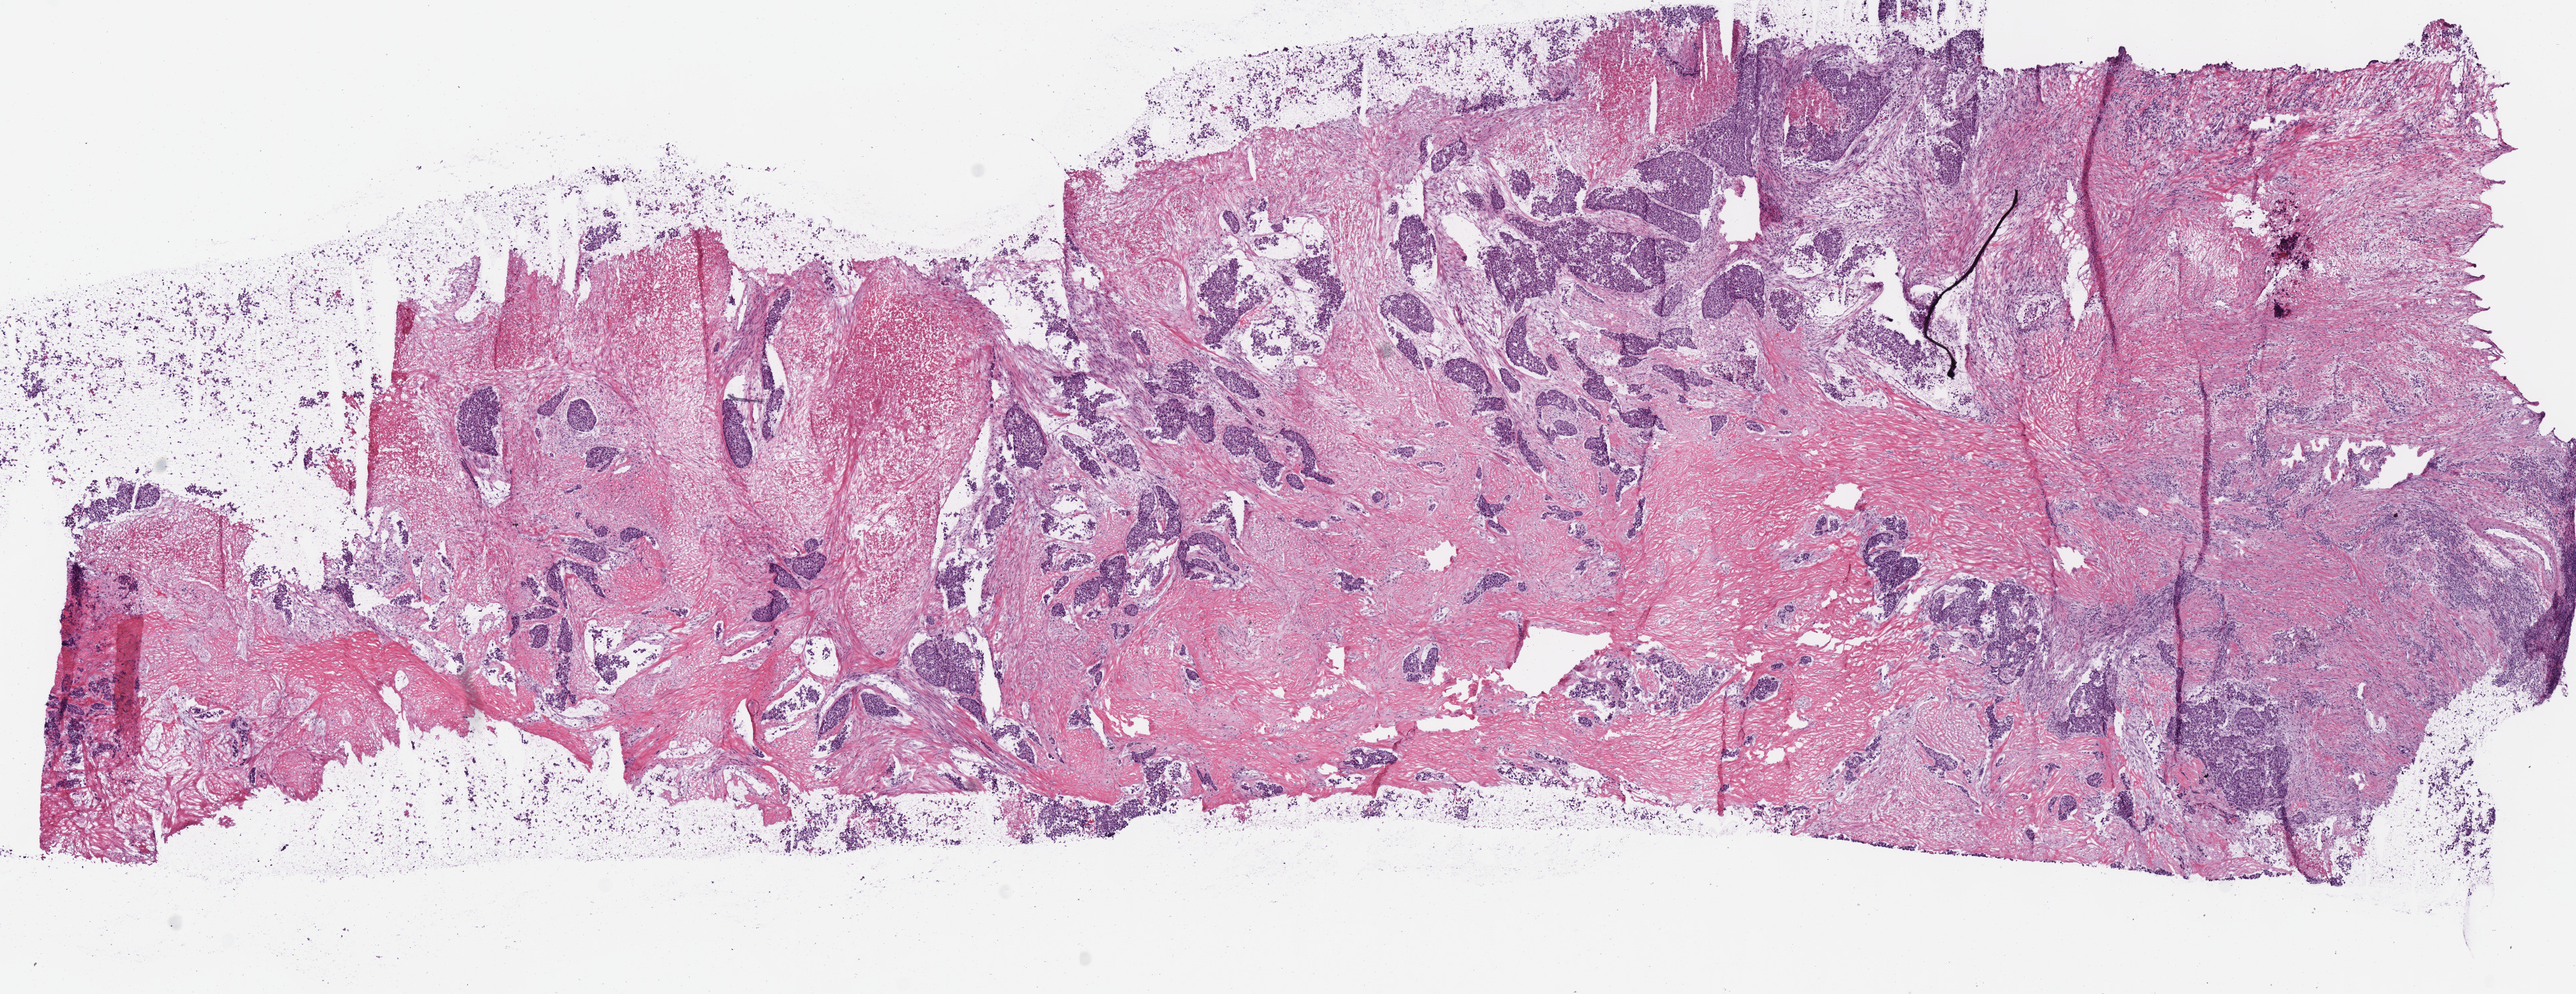
Whole-slide histology image, H&E, low-resolution overview of the scanned area, about 15.2 x 5.9 mm. Frozen section from the top of the tissue portion. Lung, primary tumour sample. Male patient; age at initial diagnosis 73 years. Composition of this section per pathologist review: tumour cells 73%, tumour nuclei 70%, normal cells 0%, stromal cells 19%, necrosis 8%. Inflammatory infiltration, as recorded: lymphocyte infiltration 15%, monocyte infiltration 0%, neutrophil infiltration 0%.
* laterality: right
* AJCC pathologic stage: IIB (7th edition)
* histologic diagnosis: Adenocarcinoma, NOS (upper lobe, lung)